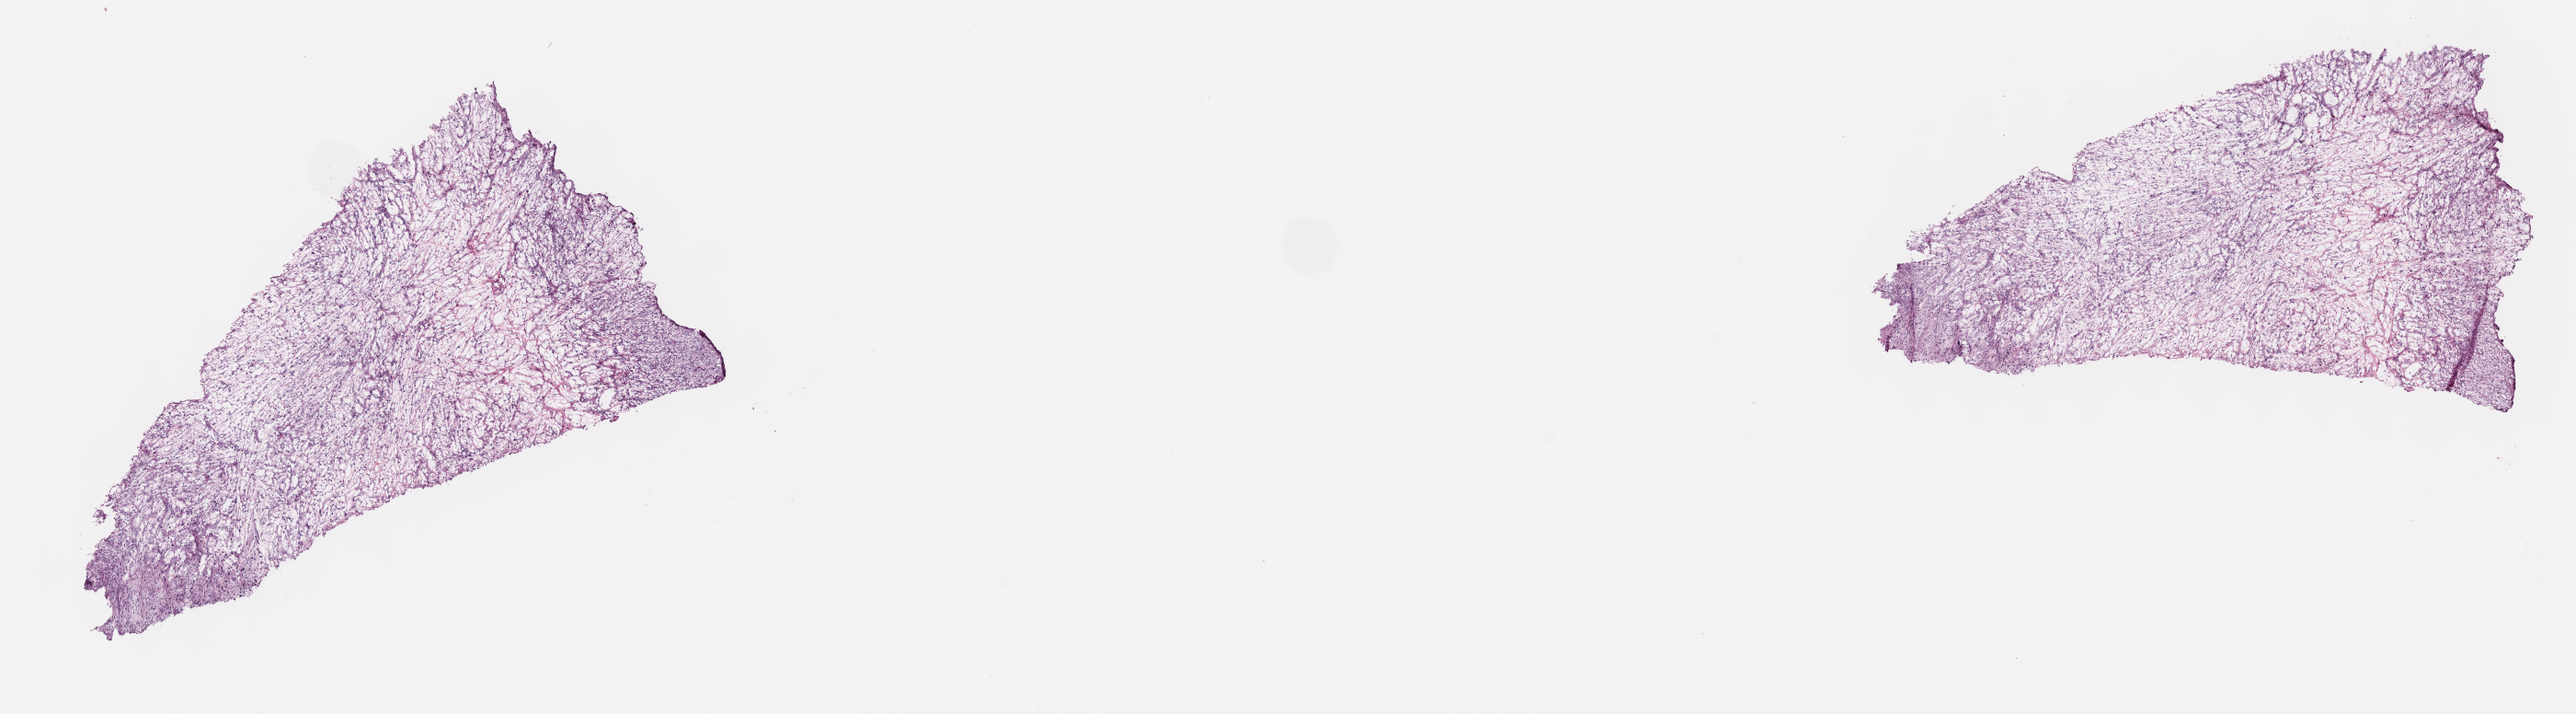
Hematoxylin and eosin (H&E) stained whole-slide image — shown as a low-resolution overview of the whole scanned area (about 22.7 x 6.3 mm); frozen section; sample: primary tumour, retroperitoneum and peritoneum. Female patient; age at initial diagnosis 79 years. Composition of this section per pathologist review: tumour cells 100%, tumour nuclei 90%, normal cells 0%, stromal cells 0%, necrosis 0%. Infiltration values recorded for this section: lymphocyte infiltration 0%, monocyte infiltration 0%, neutrophil infiltration 0%.
Histologic diagnosis: Fibromyxosarcoma (retroperitoneum).